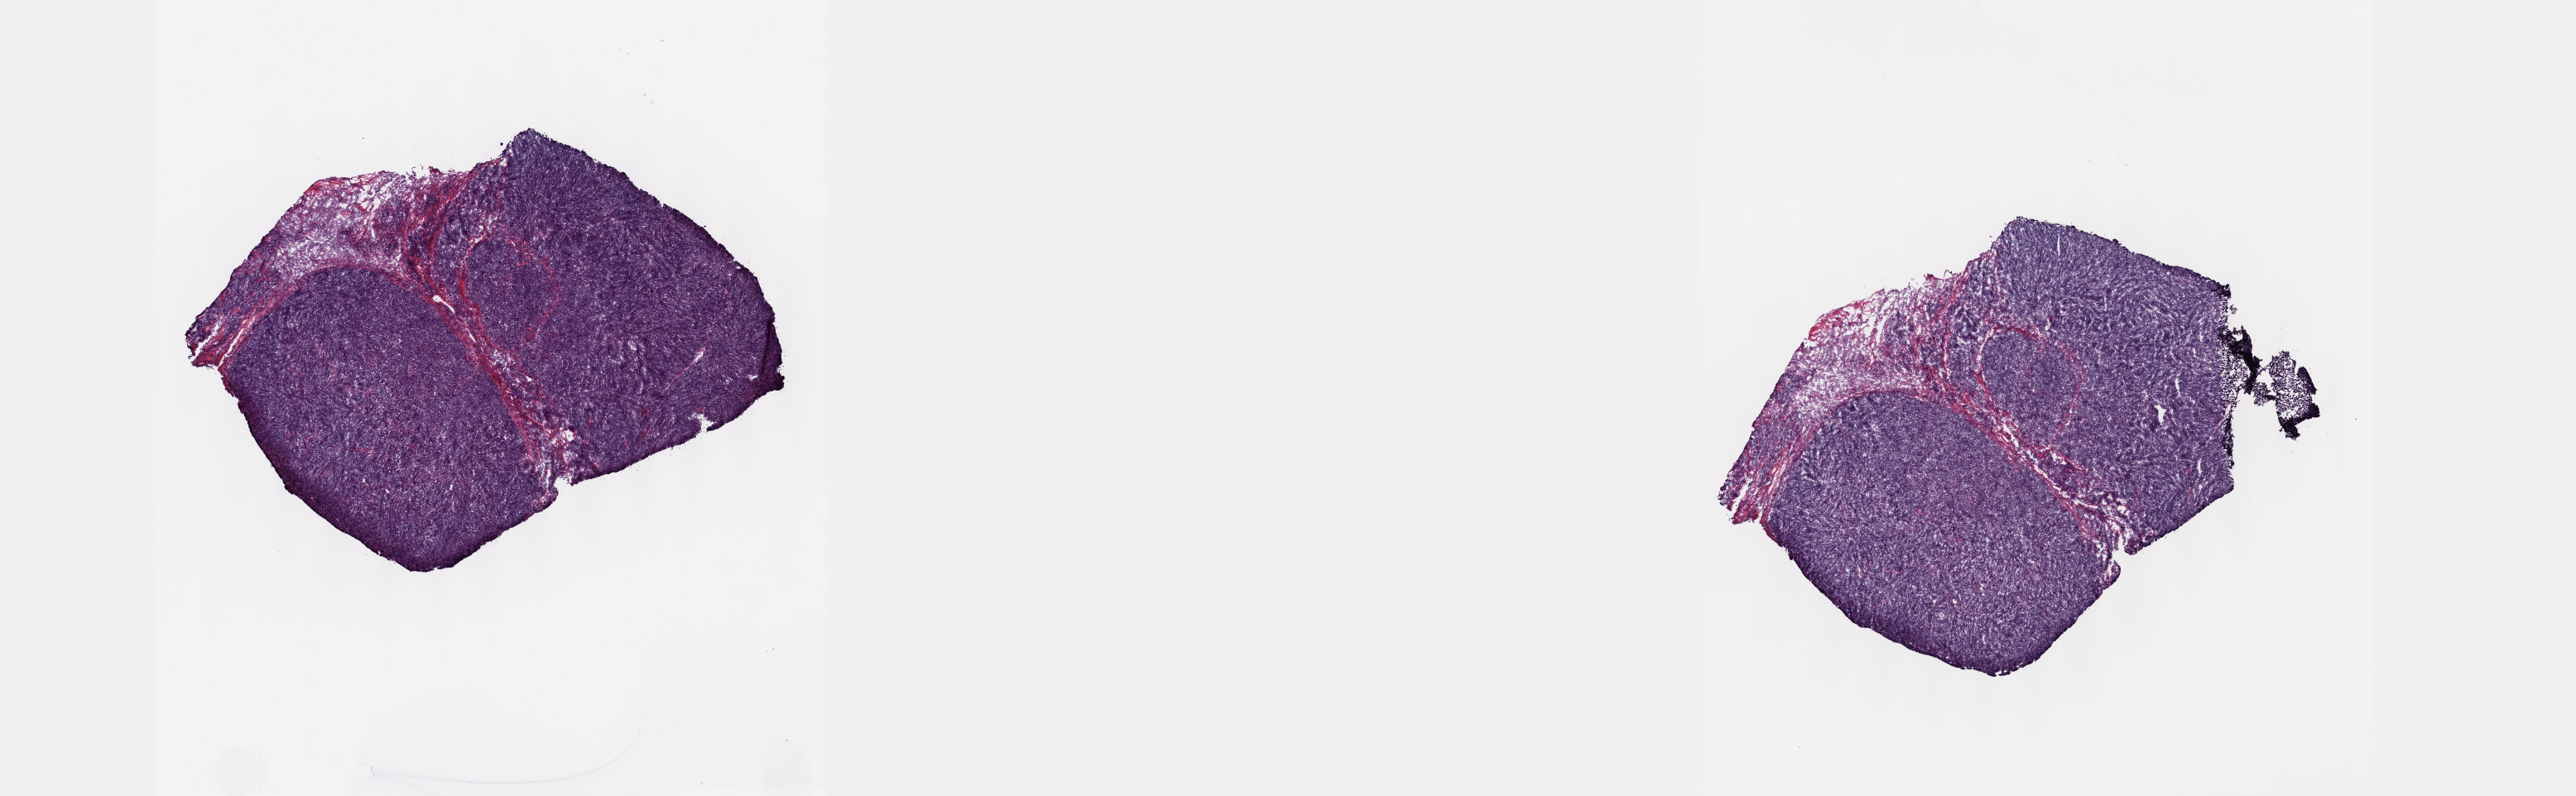
Hematoxylin and eosin (H&E) stained whole-slide image — a low-resolution overview of the entire scanned area, about 25.1 x 7.8 mm (from a 40x scan). Frozen section from the top of the tissue portion. Primary tumour sample from the thymus. Male, age 69 years at initial diagnosis. Composition of this section per pathologist review: tumour cells 95%, tumour nuclei 95%, normal cells 0%, stromal cells 5%, necrosis 0%. Infiltration values recorded for this section: lymphocyte infiltration 0%, monocyte infiltration 0%, neutrophil infiltration 0%.
Diagnosis: Thymoma, type AB, NOS.